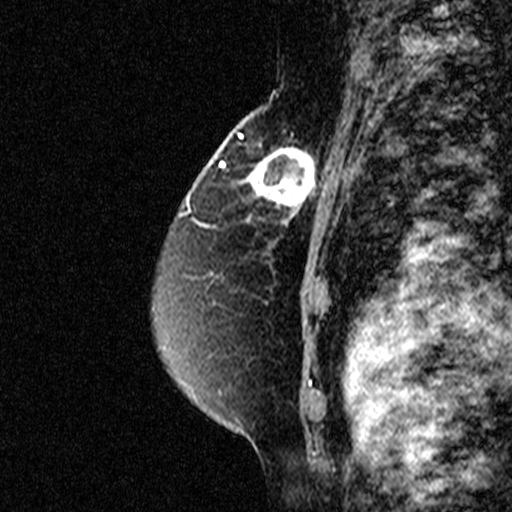
Breast MRI (dynamic contrast-enhanced), one sagittal slice. Slice 29 of 44 in the series (ordered by position). Dynamic contrast-enhanced study with each time point stored as its own series, time point 2 of 3 at this slice position (early post-contrast, ordered by acquisition time). 1.5 T. TE 4.5 ms, TR 11 ms. 3 mm slice thickness. 512 × 512 image matrix. Patient: female, 49 years. From the clinical record (not read from this slice): setting: breast cancer imaged before/during neoadjuvant chemotherapy; receptor status: triple-negative.
Outlined on this slice (semi-automatically segmented with operator editing):
- analysis volume of interest (the breast-tissue region the enhancement analysis was run in; not a lesion): bounding box <243,122,331,227> (left, top, right, bottom; pixels)
- tumour enhancement mask (voxels above the 90 % enhancement threshold inside the analysis volume of interest): <248,145,317,225>